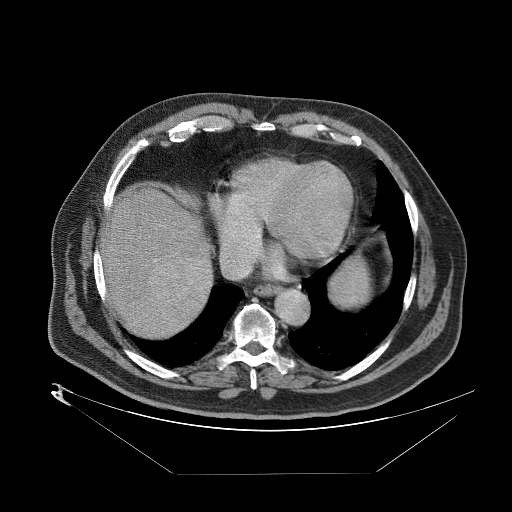
Contrast-enhanced abdominal CT (liver protocol), one axial slice. Slice 76 of 89 in the series (ordered by position). Reconstruction kernel STANDARD. 140 kVp. One of 2 acquisitions stored at this slice position. Soft-tissue window (W 400 / L 40 HU). 2.5 mm slice thickness. 512 × 512 image matrix. Case-level facts recorded for this patient, not image findings: diagnosis: hepatocellular carcinoma (patient treated with transarterial chemoembolisation; whether this scan precedes or follows treatment is not stated here); TNM stage (as recorded): Stage-II; Child-Pugh class: B; tumour differentiation: moderately differentiated.
Annotated regions visible in this slice (semi-automatic segmentation, software-assisted and operator-edited):
- abdominal aorta: bounding box [x1, y1, x2, y2] px = [274, 289, 309, 324]
- liver parenchyma outside the tumour (the mass and vessels are separate outlines, so this box may not span the whole liver): [100, 184, 208, 328]
- mass: [150, 256, 204, 311]
- liver vessels: [142, 259, 207, 304]